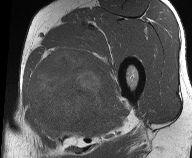
MRI of an extremity soft-tissue mass, one axial slice. MR volume resampled by the dataset authors to the PET/CT grid (not the native acquisition matrix). 3.27 mm slice thickness. 192 × 158 image matrix, field of view 187 × 154 mm. Male patient. From the clinical record (not read from this slice): histological type: pleiomorphic liposarcoma; grade: high; site of the primary tumour: left thigh.
Annotated regions visible in this slice (expert contour drawn on MRI and transferred to this co-registered scan by the dataset authors):
- gross tumour volume including surrounding oedema: box from (x=27, y=46) to (x=115, y=140) px
- gross tumour volume (mass): (x=27, y=48)–(x=113, y=131)